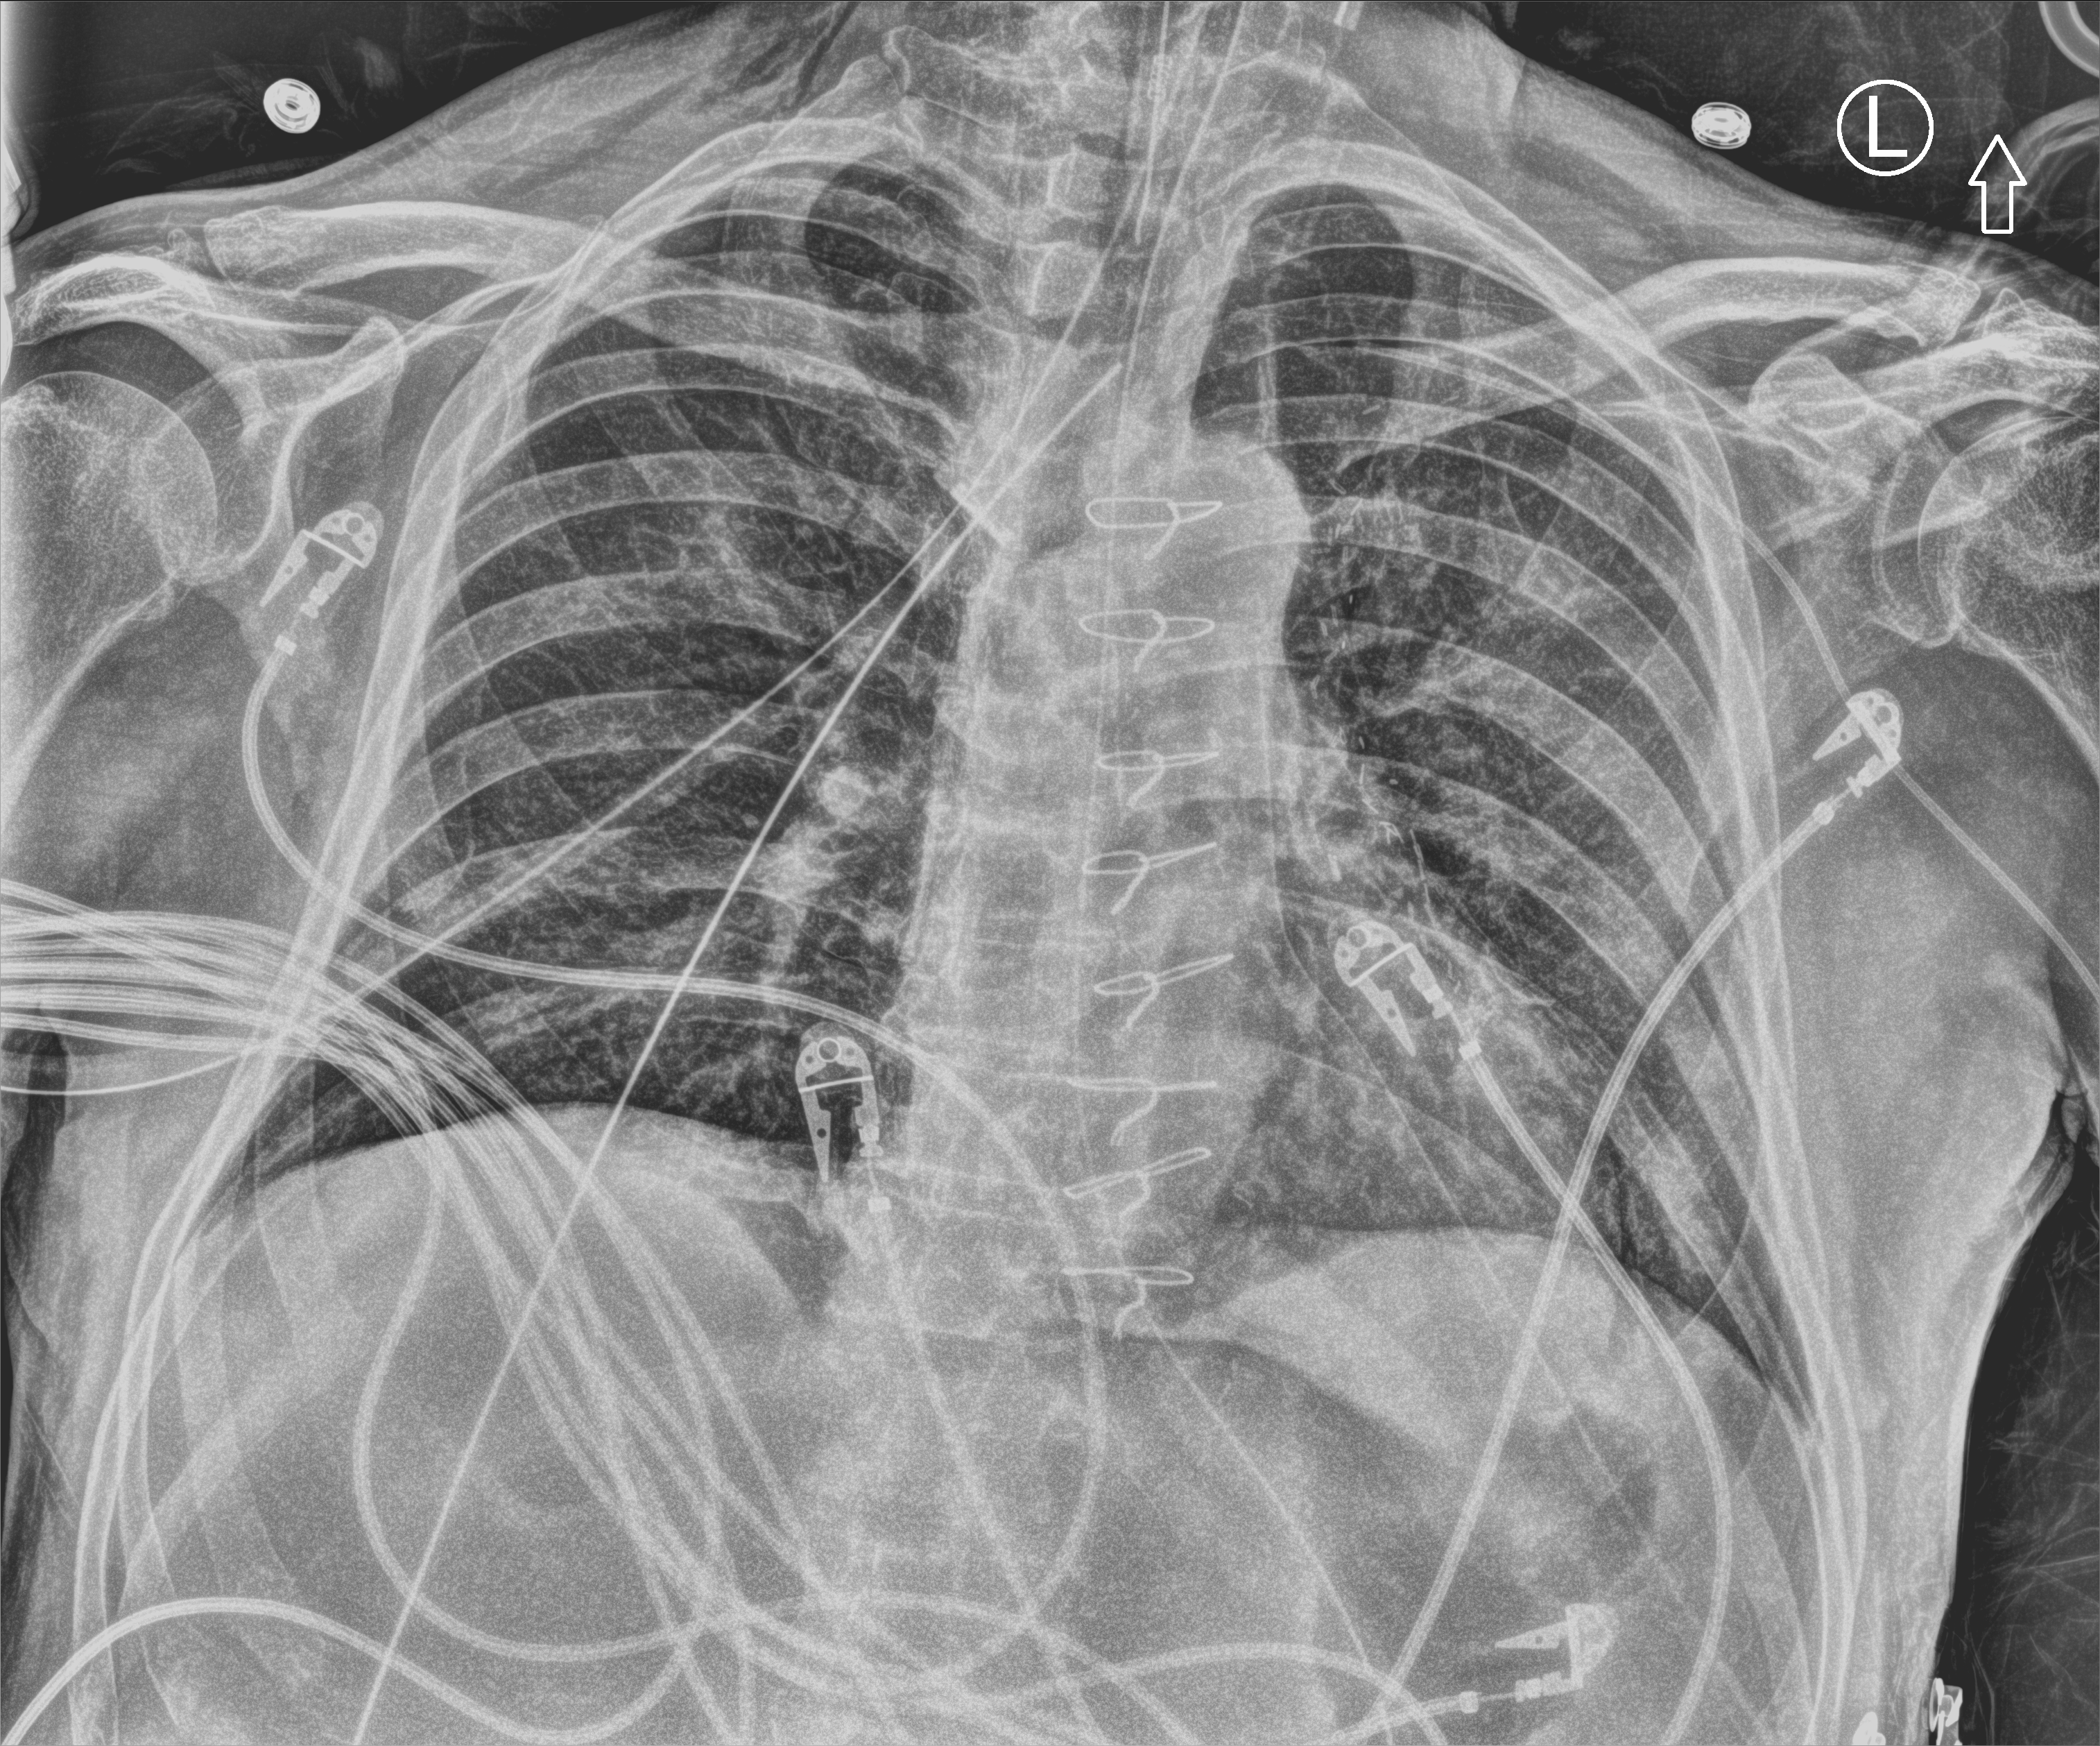
Chest X-ray (portable), anteroposterior (AP) projection. Patient hospitalised with COVID-19; male, aged 60–74 years.
Hospital-stay facts (about this admission, not read from this image; timing relative to this image not recorded):
- smoking status (admission record): never
- mechanically ventilated during this hospital stay: yes
- admitted to intensive care during this hospital stay: yes